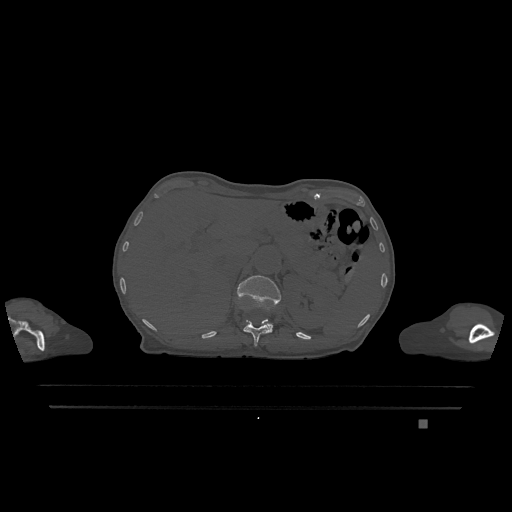
CT including the spine, one axial slice; position 511 of 1317 along the scan axis; bone window (W 1800 / L 400 HU); 512 × 512 image matrix, field of view 500 × 500 mm. Female patient, age 74 years. Case-level facts recorded for this patient, not image findings: primary cancer: lung; vertebrae with lytic lesions (as recorded): T1, T4, T5, T6, L4, L5.
Structures marked on this image (semi-automatically segmented with operator editing):
- L1 vertebra: box from (x=237, y=275) to (x=281, y=332) px
- T12 vertebra: (x=243, y=319)–(x=271, y=346)